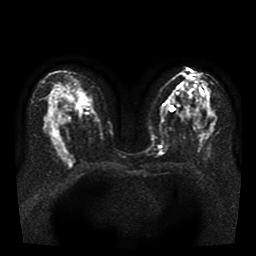
Breast MRI, one axial slice. Position 21 of 41 along the scan axis. Diffusion-weighted series; image 2 of 4 stored at this slice position (different b-values; order by instance number). 1.5 T. 5 mm slice thickness. 256 × 256 image matrix. Female patient.
Outlined on this slice (expert manual segmentation):
- tumour on diffusion-weighted imaging: bounding box [x1, y1, x2, y2] px = [74, 105, 84, 115]